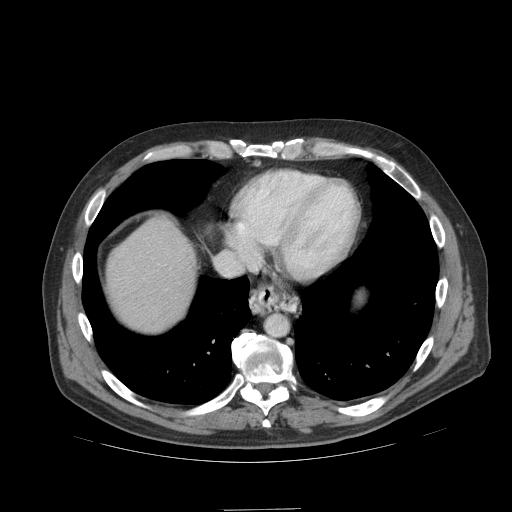
Contrast-enhanced abdominal CT (liver protocol), one axial slice; position 92 of 99 along the scan axis; reconstruction kernel STANDARD; 140 kVp; soft-tissue window (W 400 / L 40 HU); 2.5 mm slice thickness; 512 × 512 image matrix. Case-level facts recorded for this patient, not image findings: diagnosis: hepatocellular carcinoma (patient treated with transarterial chemoembolisation; whether this scan precedes or follows treatment is not stated here); TNM stage (as recorded): Stage-I; Child-Pugh class: A; tumour differentiation: no biopsy; tumour nodularity: uninodular.
Outlined on this slice (semi-automatic segmentation, software-assisted and operator-edited):
- abdominal aorta: bounding box (x1, y1, x2, y2) in pixels: (265, 314, 288, 335)
- liver parenchyma outside the tumour (the mass and vessels are separate outlines, so this box may not span the whole liver): (106, 218, 194, 330)